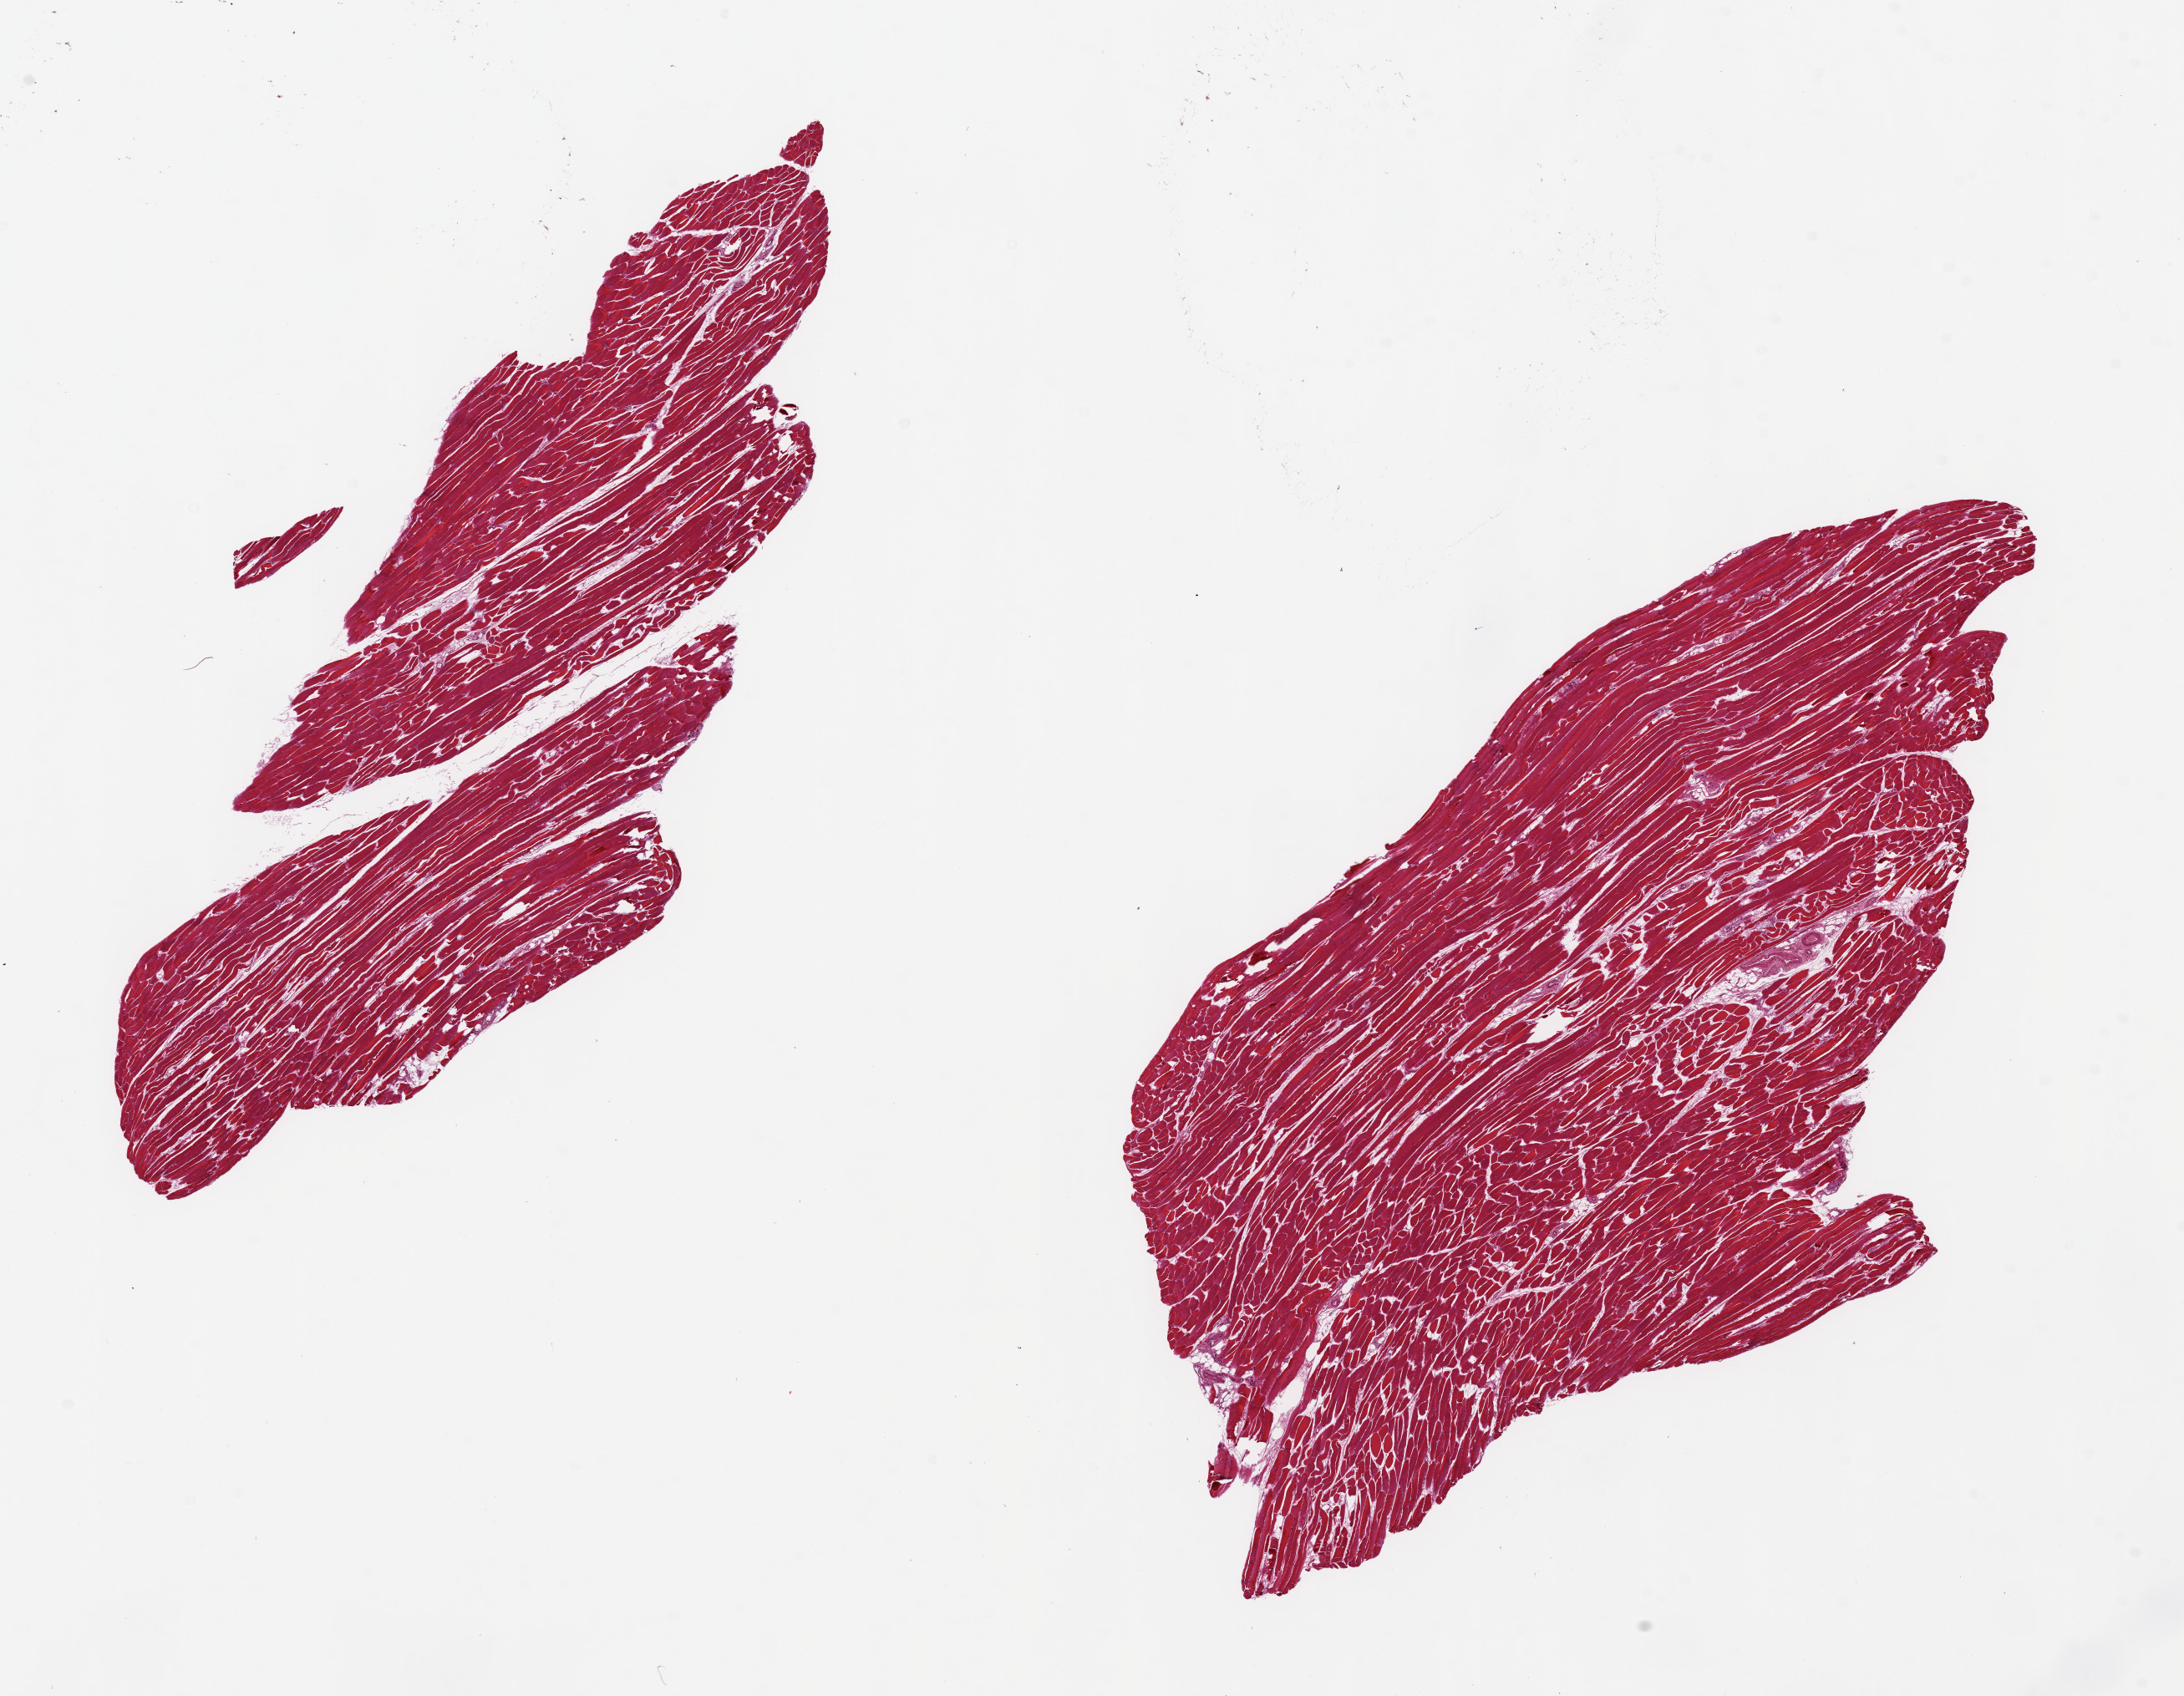
H&E whole-slide image, low-resolution overview of the scanned area, about 20.7 x 16.1 mm, PAXgene-fixed paraffin-embedded (PFPE) section, sampled site (target tissue): skeletal muscle, tissue donor sample. Donor: female.
Pathologist's review note for this sample: 2 pieces ~10x4mm. No interstitial fat.